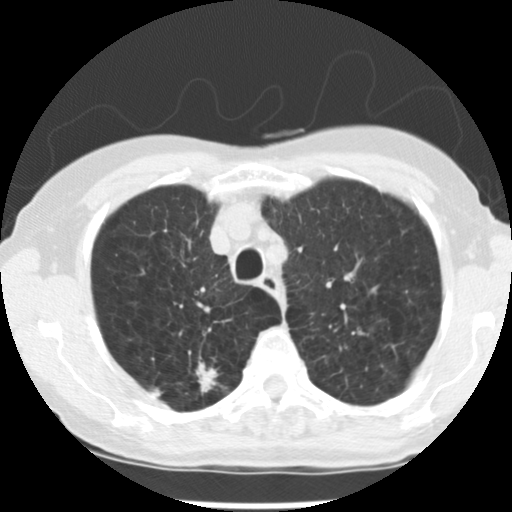
Low-dose screening chest CT, axial slice. Baseline annual screen. Lung window (W 1500 / L -600 HU). 2.5 mm slice thickness. 120 kVp. Slice 52 of 265 in the series. 512 × 512 image matrix, field of view 300 × 300 mm. Female participant, aged 72 years at enrolment. Current smoker at enrolment.
Expert-annotated lung lesion, box from (x=183, y=357) to (x=236, y=406) px. The screening reader recorded 3 non-calcified nodules or masses ≥4 mm on this exam (right upper lobe, left upper lobe, left lower lobe); which of them this box marks is not recorded. Official screen result: positive, change unspecified: nodule(s) >= 4 mm or enlarging nodule(s), mass(es), or other non-specific abnormalities suspicious for lung cancer. Participant outcome: lung cancer diagnosed 50 days after this screen — adenocarcinoma, NOS, right upper lobe, moderately differentiated (G2), stage IB (AJCC 6th edition), 22 mm at pathology.